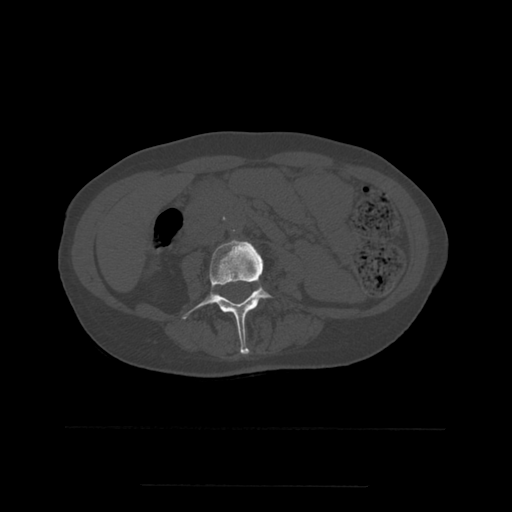
CT including the spine, one axial slice. Slice 187 of 544 in the series (ordered by position). Bone window (W 1800 / L 400 HU). 512 × 512 image matrix. Patient age 58 years. Case-level facts recorded for this patient, not image findings: primary cancer: lung.
Annotated regions visible in this slice (semi-automatic segmentation, software-assisted and operator-edited):
- L3 vertebra: box from (x=182, y=240) to (x=273, y=354) px